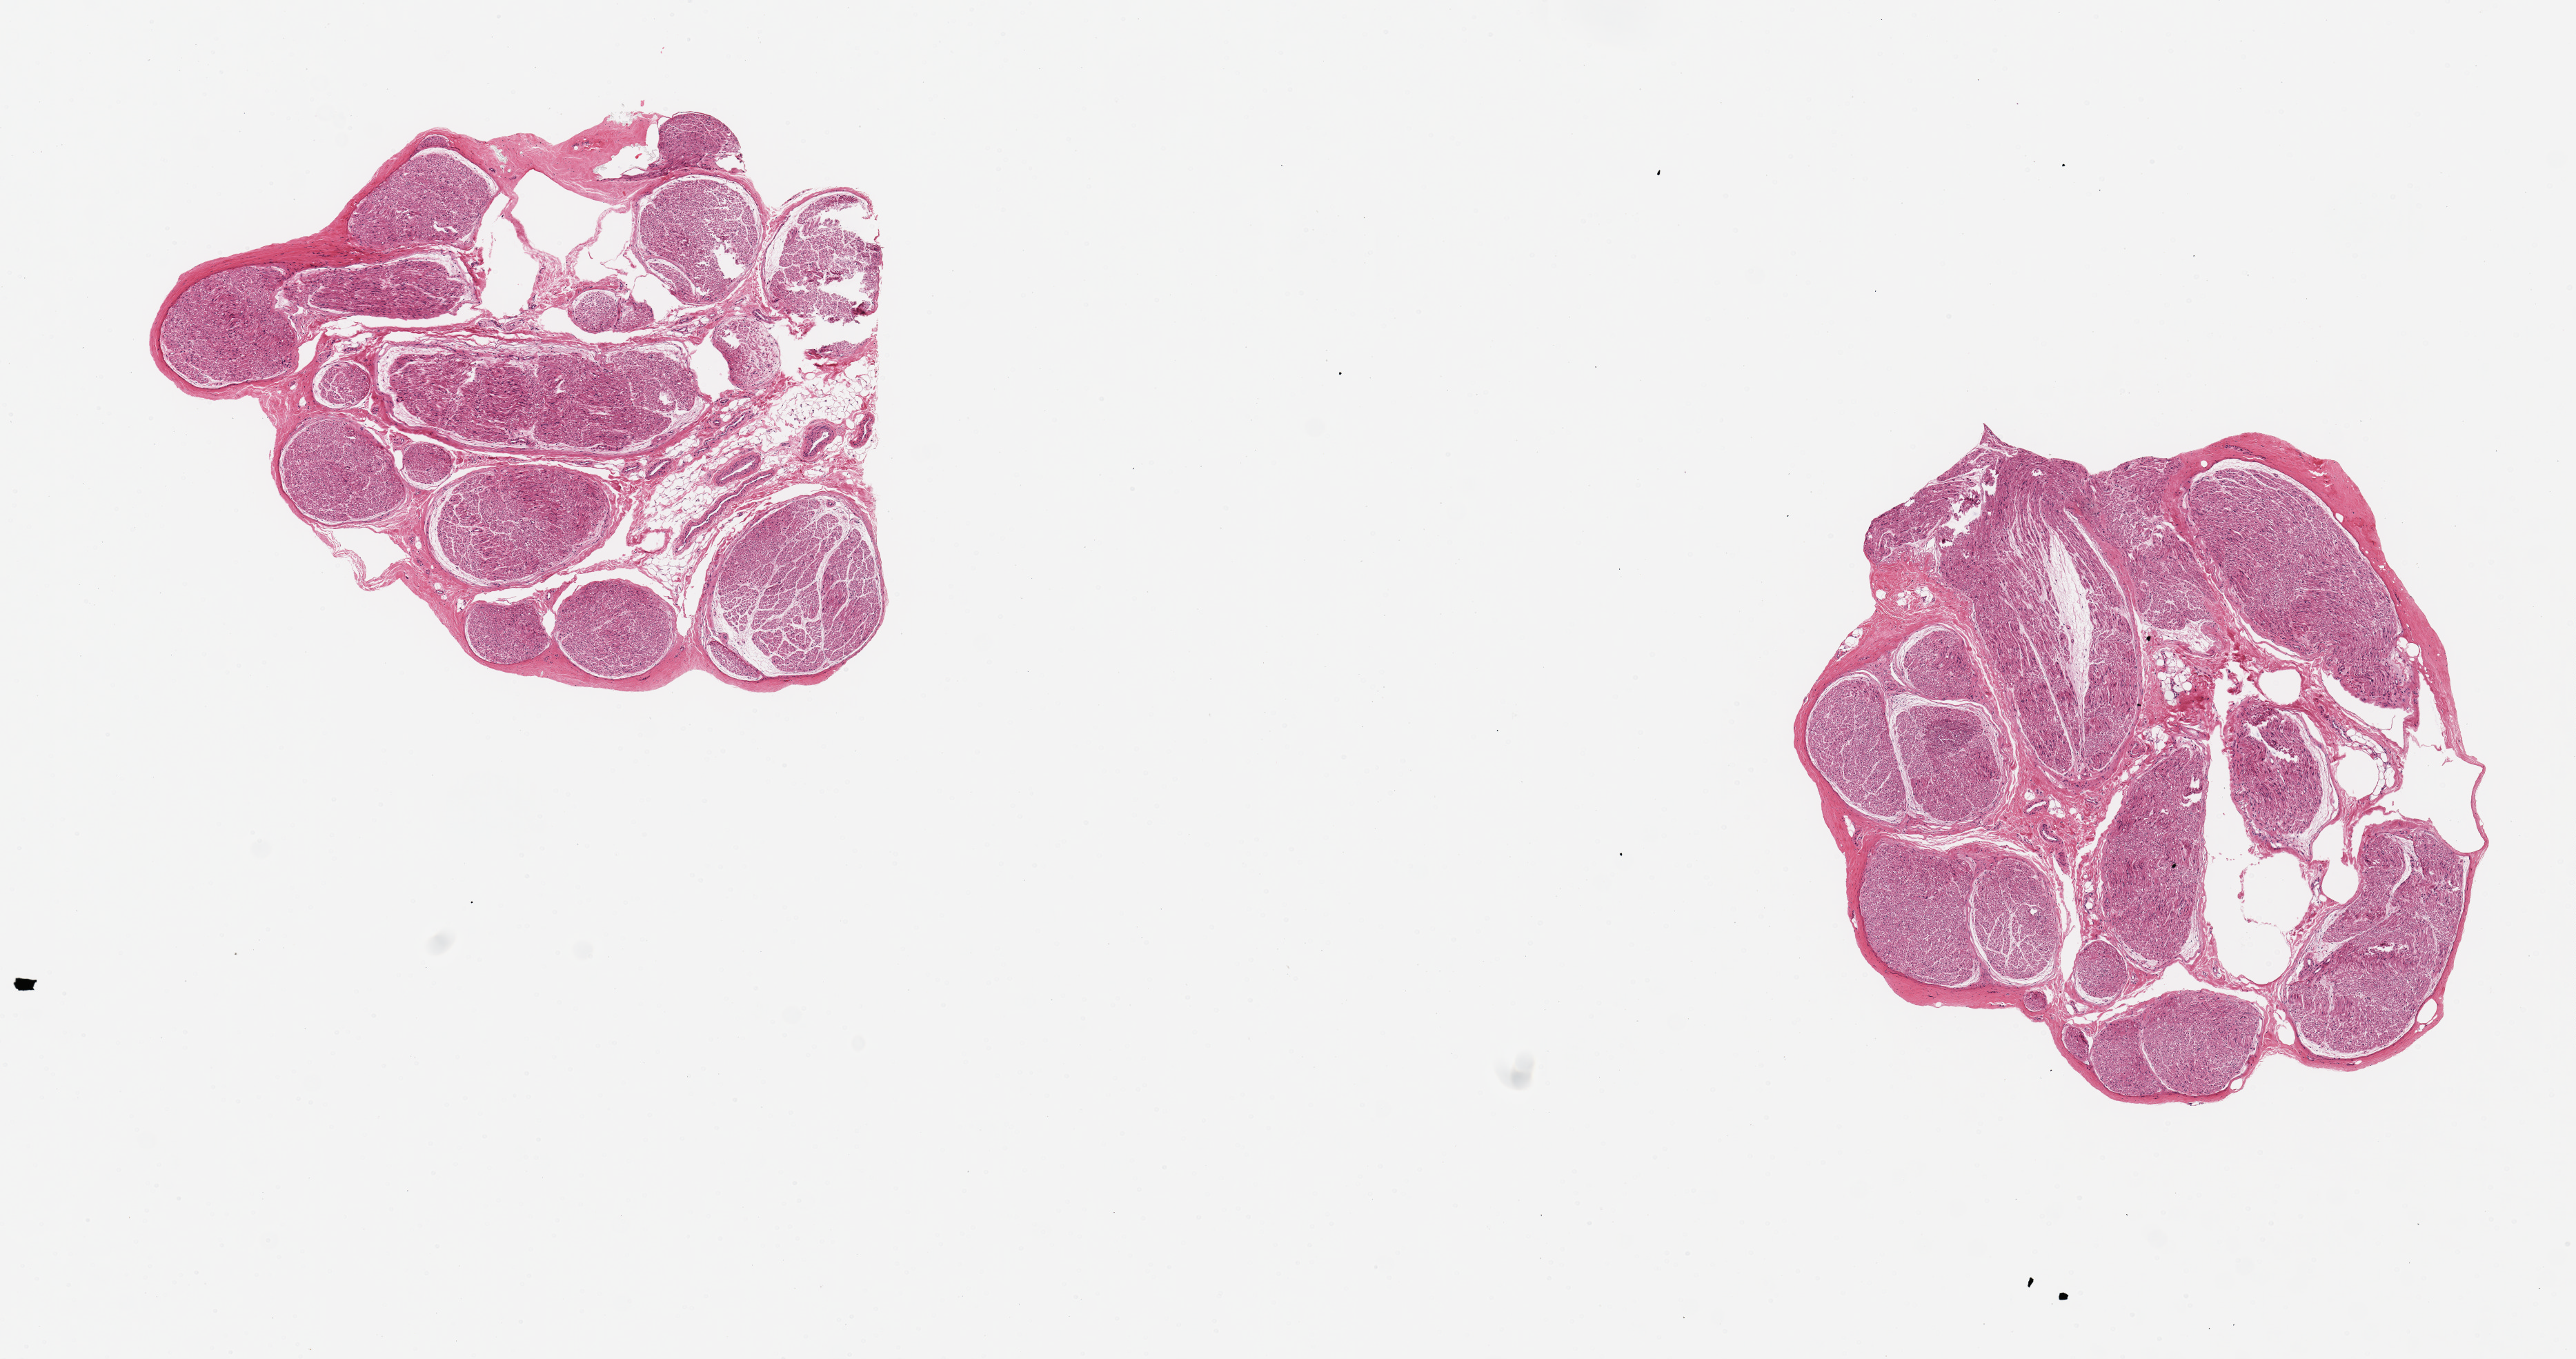
Digitized H&E-stained section — whole scanned area (about 14.8 x 7.8 mm) shown as a low-resolution overview. PAXgene-fixed, paraffin-embedded tissue. Sampled site (target tissue): tibial nerve. Tissue donor sample. Female donor.
Reviewer comment on this tissue sample: 2 pieces 4x3 & 3x3 mm; <10% adipose.